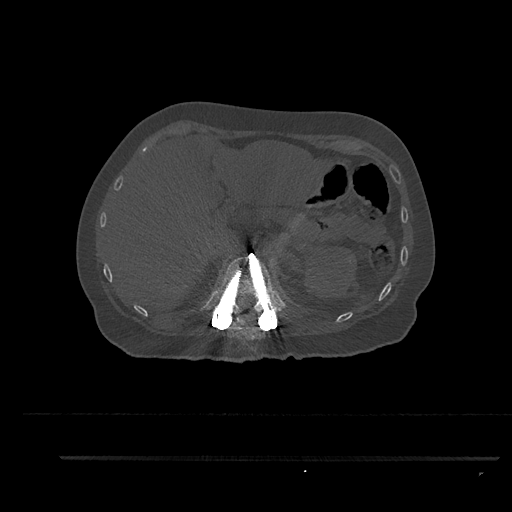
CT including the spine, one axial slice. Slice 275 of 797 in the series (ordered by position). Reconstruction kernel Br40s/3. Bone window (W 1800 / L 400 HU). 512 × 512 image matrix, field of view 408 × 408 mm. Female patient, age 44 years. Case-level facts recorded for this patient, not image findings: primary cancer: renal.
Structures marked on this image (semi-automatically segmented with operator editing):
- T11 vertebra: bounding box (x1, y1, x2, y2) in pixels: (232, 317, 251, 339)
- T12 vertebra: (213, 256, 282, 320)